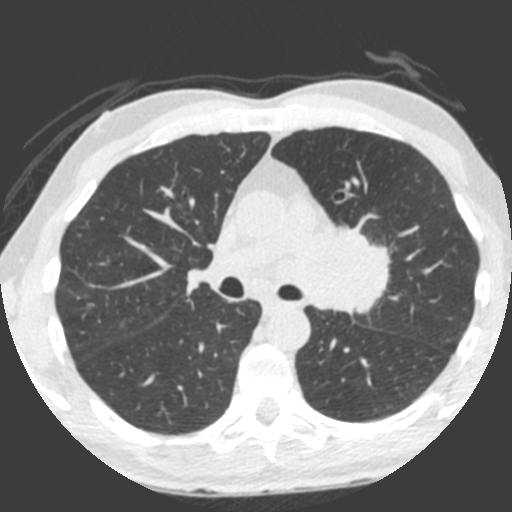
Low-dose screening chest CT, one axial slice; 120 kVp; lung window (W 1500 / L -600 HU); 2 mm slice thickness; 512 × 512 image matrix, field of view 315 × 315 mm.
Annotated regions visible in this slice (manually delineated by an expert):
- lesion 1 (tumor, upper lobe of left lung): box from (x=313, y=227) to (x=391, y=316) px